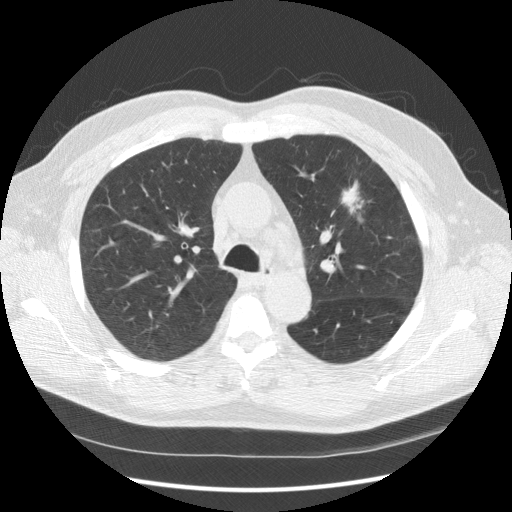
Low-dose screening chest CT, one axial slice. Position 107 of 157 along the scan axis. 120 kVp. Lung window (W 1500 / L -600 HU). 512 × 512 image matrix, field of view 370 × 370 mm.
Structures marked on this image (expert manual segmentation):
- lesion 1 (tumor, upper lobe of left lung): box from (x=341, y=182) to (x=365, y=225) px